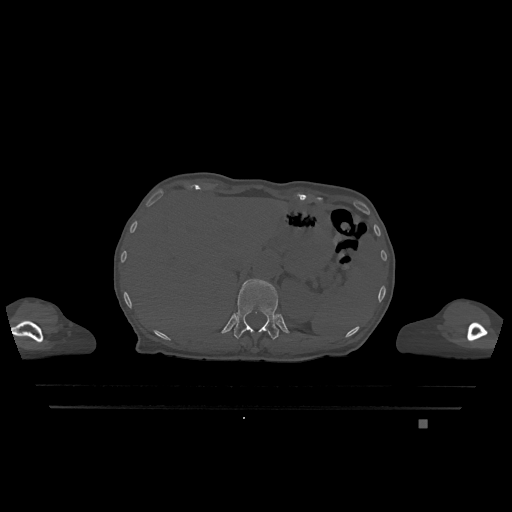
CT including the spine, one axial slice. Position 539 of 1317 along the scan axis. Bone window (W 1800 / L 400 HU). 0.5 mm slice thickness. 512 × 512 image matrix, field of view 500 × 500 mm. Patient: female, 74 years. From the clinical record (not read from this slice): primary cancer: lung.
Outlined on this slice (semi-automatically segmented with operator editing):
- T12 vertebra: bounding box (x1, y1, x2, y2) in pixels: (234, 279, 279, 340)